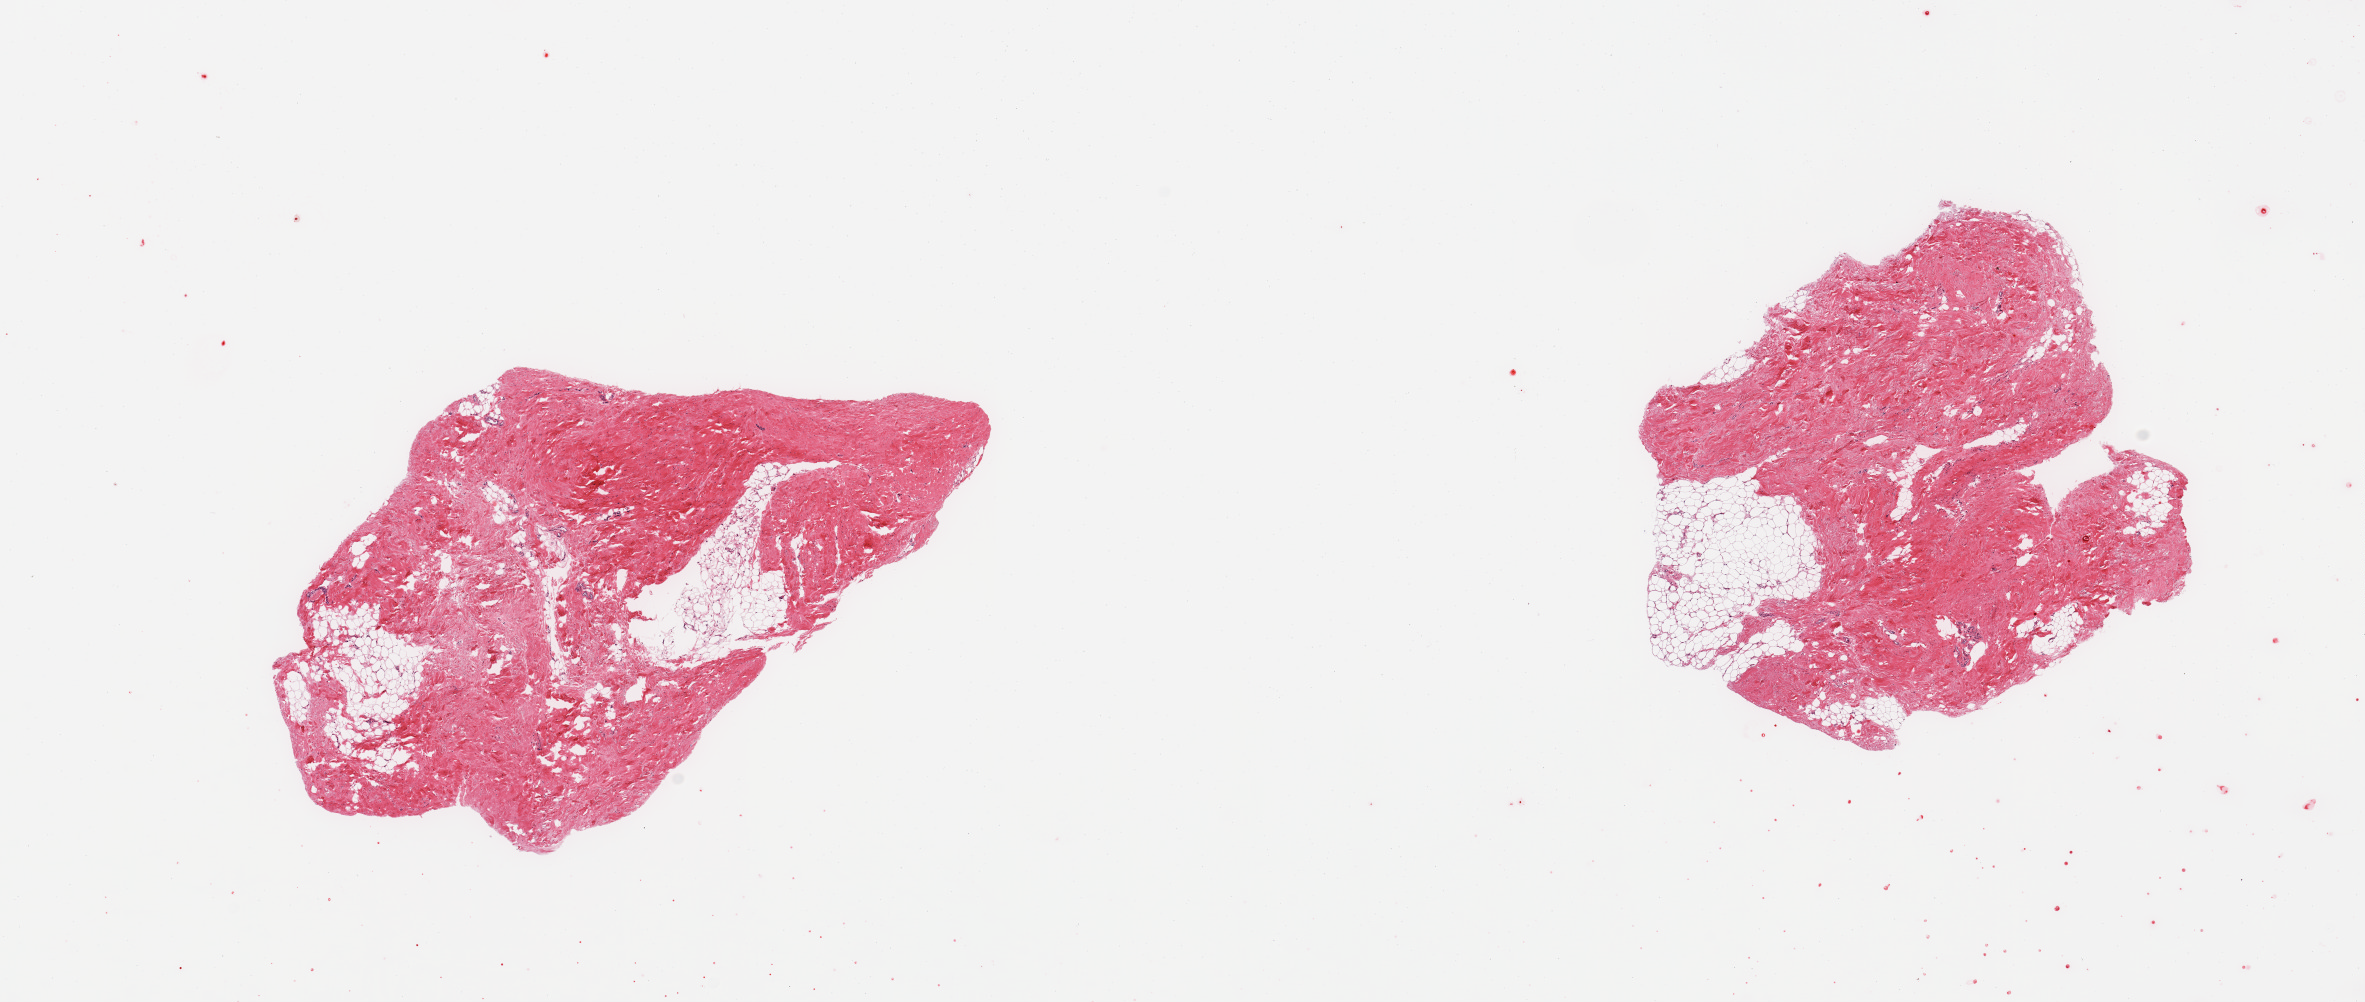
Whole-slide image, haematoxylin and eosin stain — whole scanned area (about 18.7 x 7.9 mm) shown as a low-resolution overview. PAXgene-fixed paraffin-embedded (PFPE) section. Target tissue: breast. Donor tissue sample. Male donor.
• reviewer comment on this tissue sample: 2 pieces; fibrofatty tissue without mammary ducts